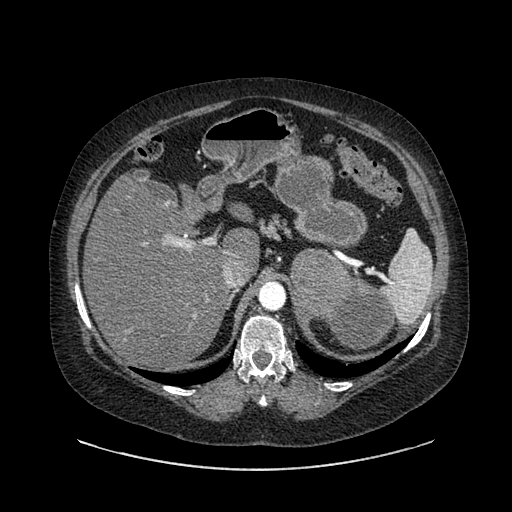
Contrast-enhanced abdominal CT, one axial slice. Reconstruction kernel SOFT. Intravenous contrast given. Soft-tissue window (W 400 / L 40 HU). 0.62 mm slice thickness. 512 × 512 image matrix, field of view 460 × 460 mm. Patient: female, 61 years. From the clinical record (not read from this slice): diagnosis: adrenocortical carcinoma; tumour side: left adrenal; tumour size at pathology: 13 cm; Ki-67 index: 79 %; stage (as recorded): 2.
Outlined on this slice (semi-automatically segmented with operator editing):
- mass: bounding box [x1, y1, x2, y2] px = [291, 253, 392, 349]